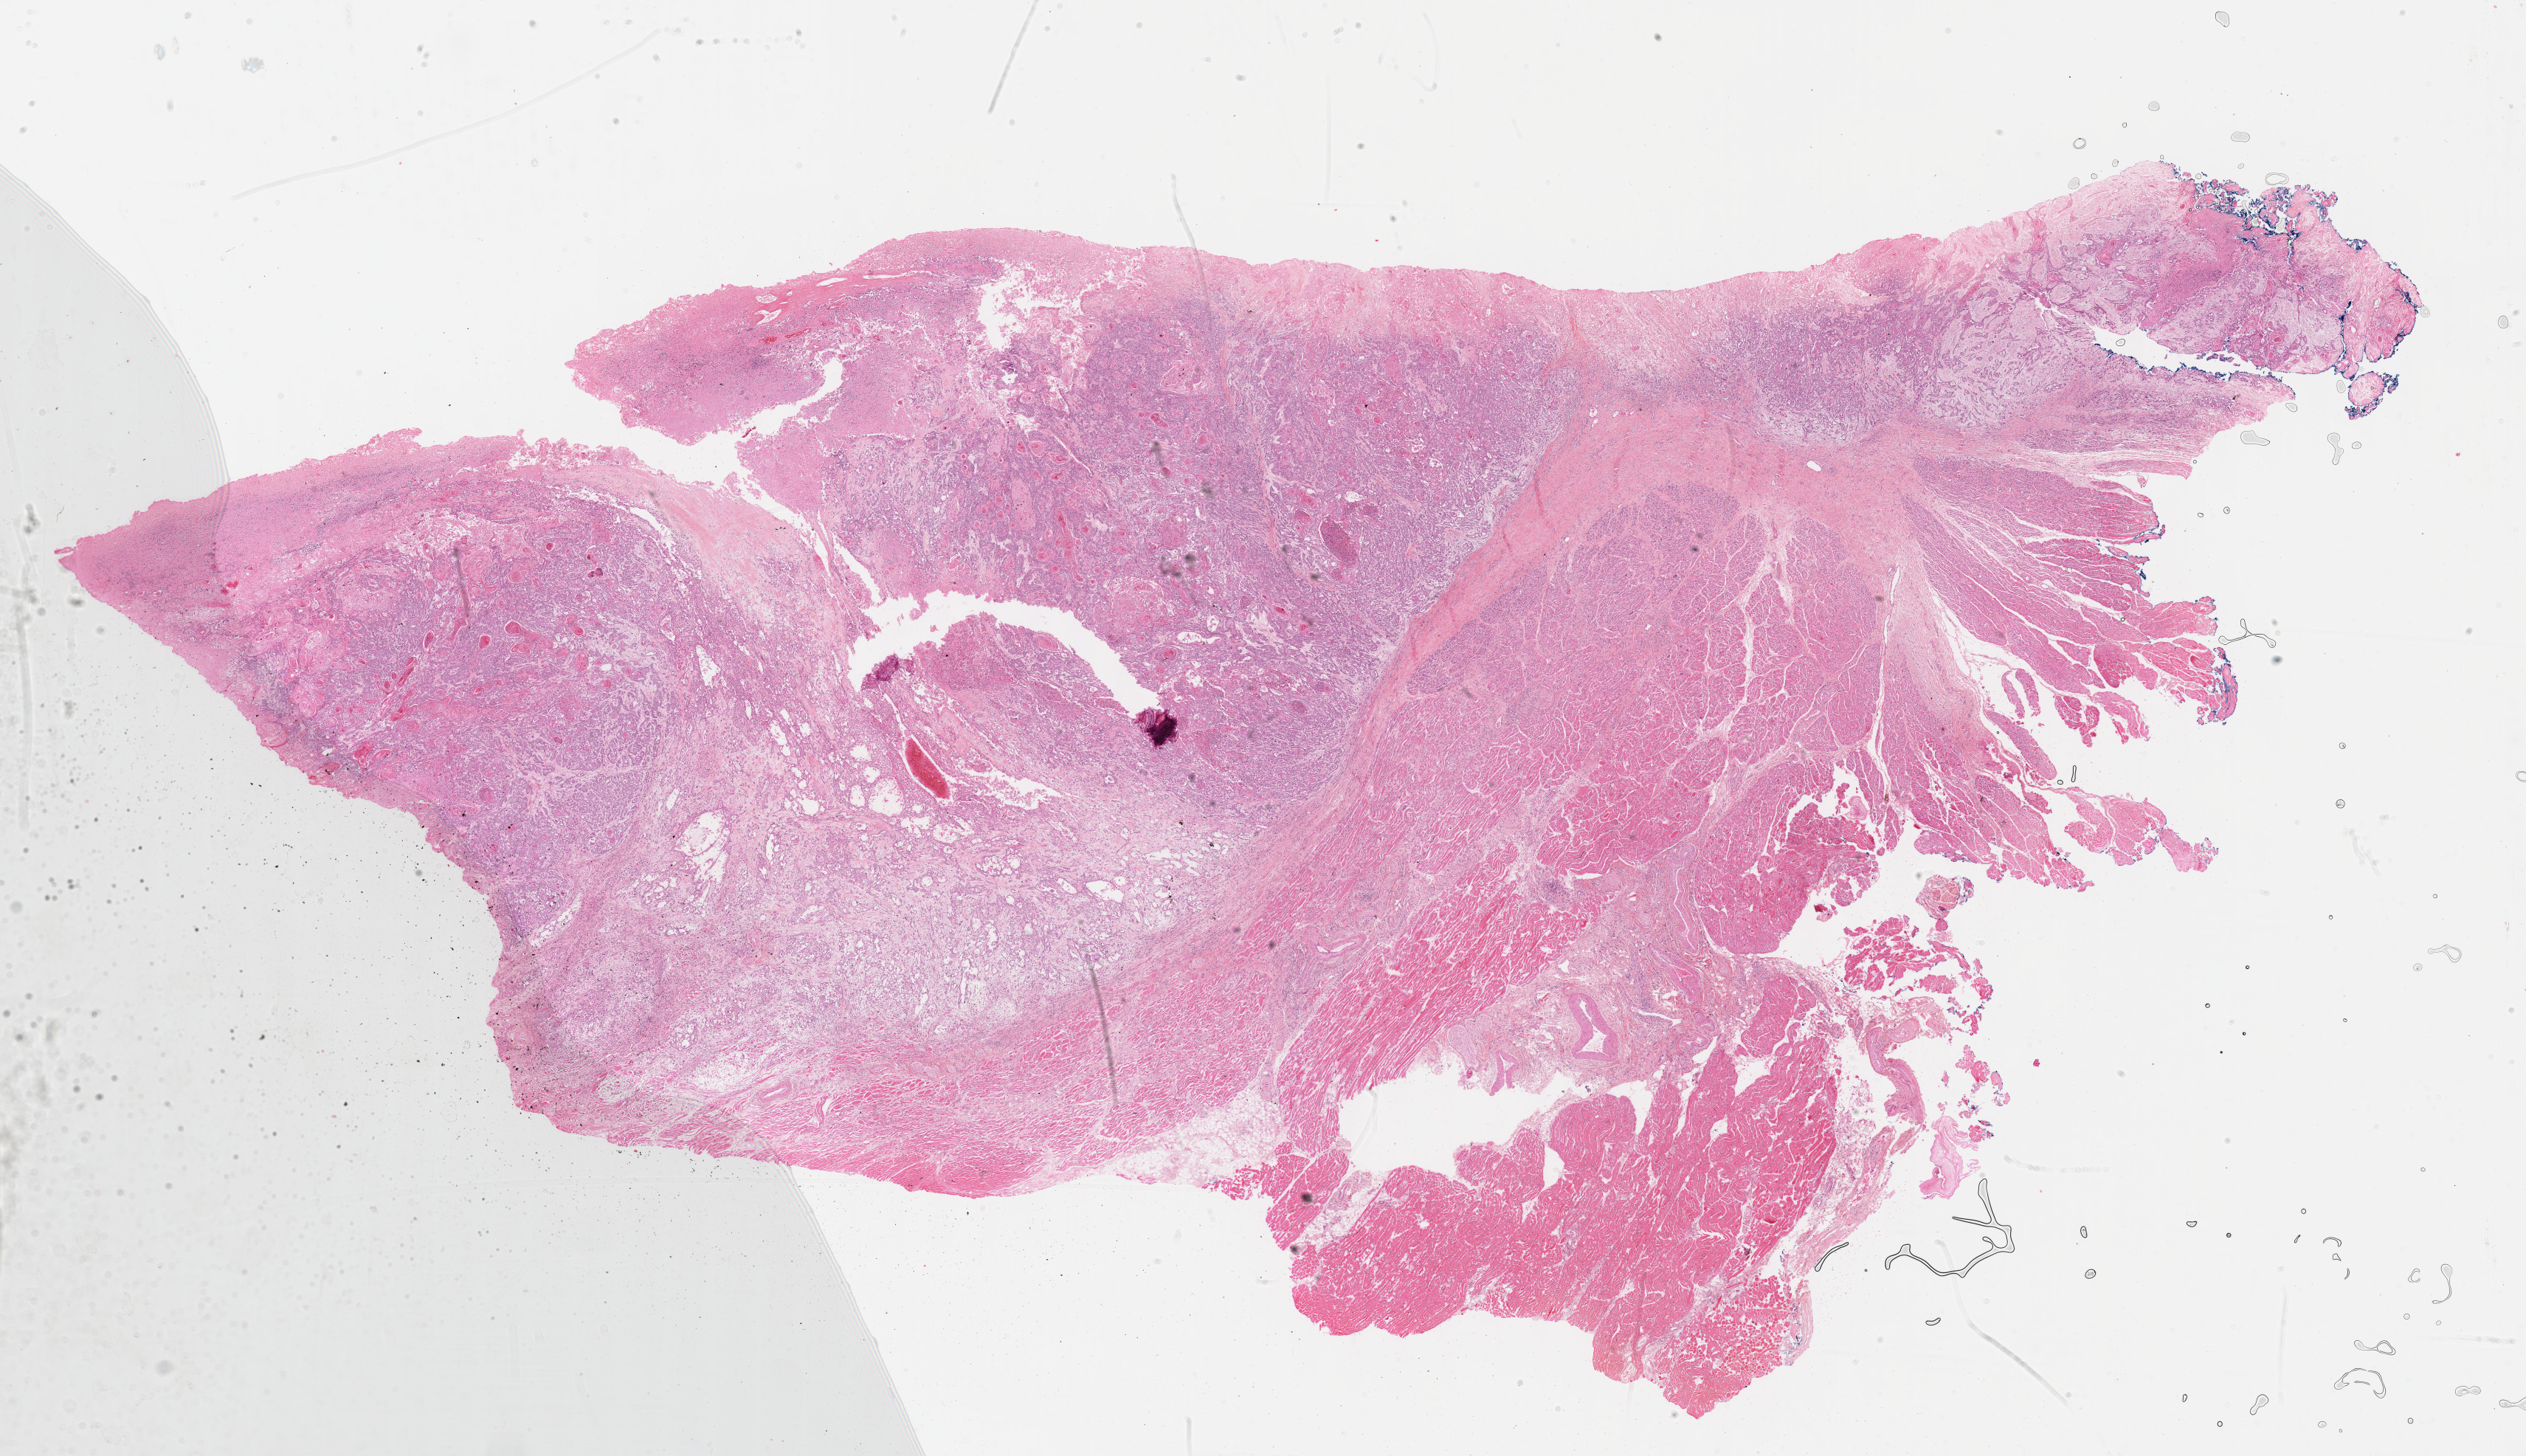
Digitized H&E-stained tissue section (whole slide), low-resolution overview of the scanned area, about 27.7 x 15.9 mm (acquisition: 40x scan), FFPE section, head and neck, primary tumour sample. Patient: male, age at initial diagnosis 49 years.
Histologic diagnosis: Squamous cell carcinoma, NOS (overlapping lesion of lip, oral cavity and pharynx).